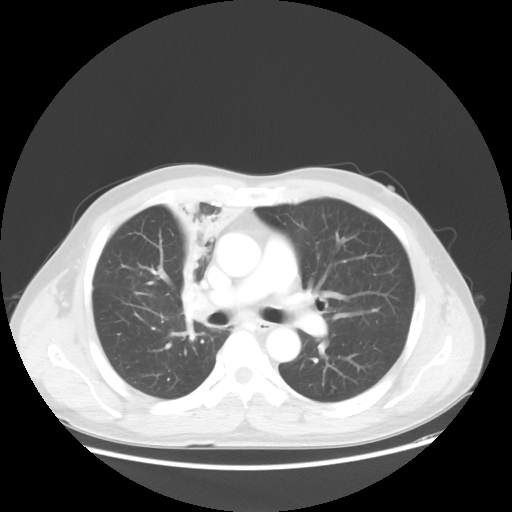
Chest CT, one axial slice; slice 33 of 56 in the series (ordered by position); lung window (W 1500 / L -600 HU); 512 × 512 image matrix, field of view 398 × 398 mm. Male patient, age 60 years. Case-level facts recorded for this patient, not image findings: clinical TNM (as recorded): T2a N1 M0.
Annotated regions visible in this slice (bounding box drawn by a radiologist):
- lung tumour (recorded histology: squamous cell carcinoma): bounding box (x1, y1, x2, y2) in pixels: (163, 196, 239, 285)